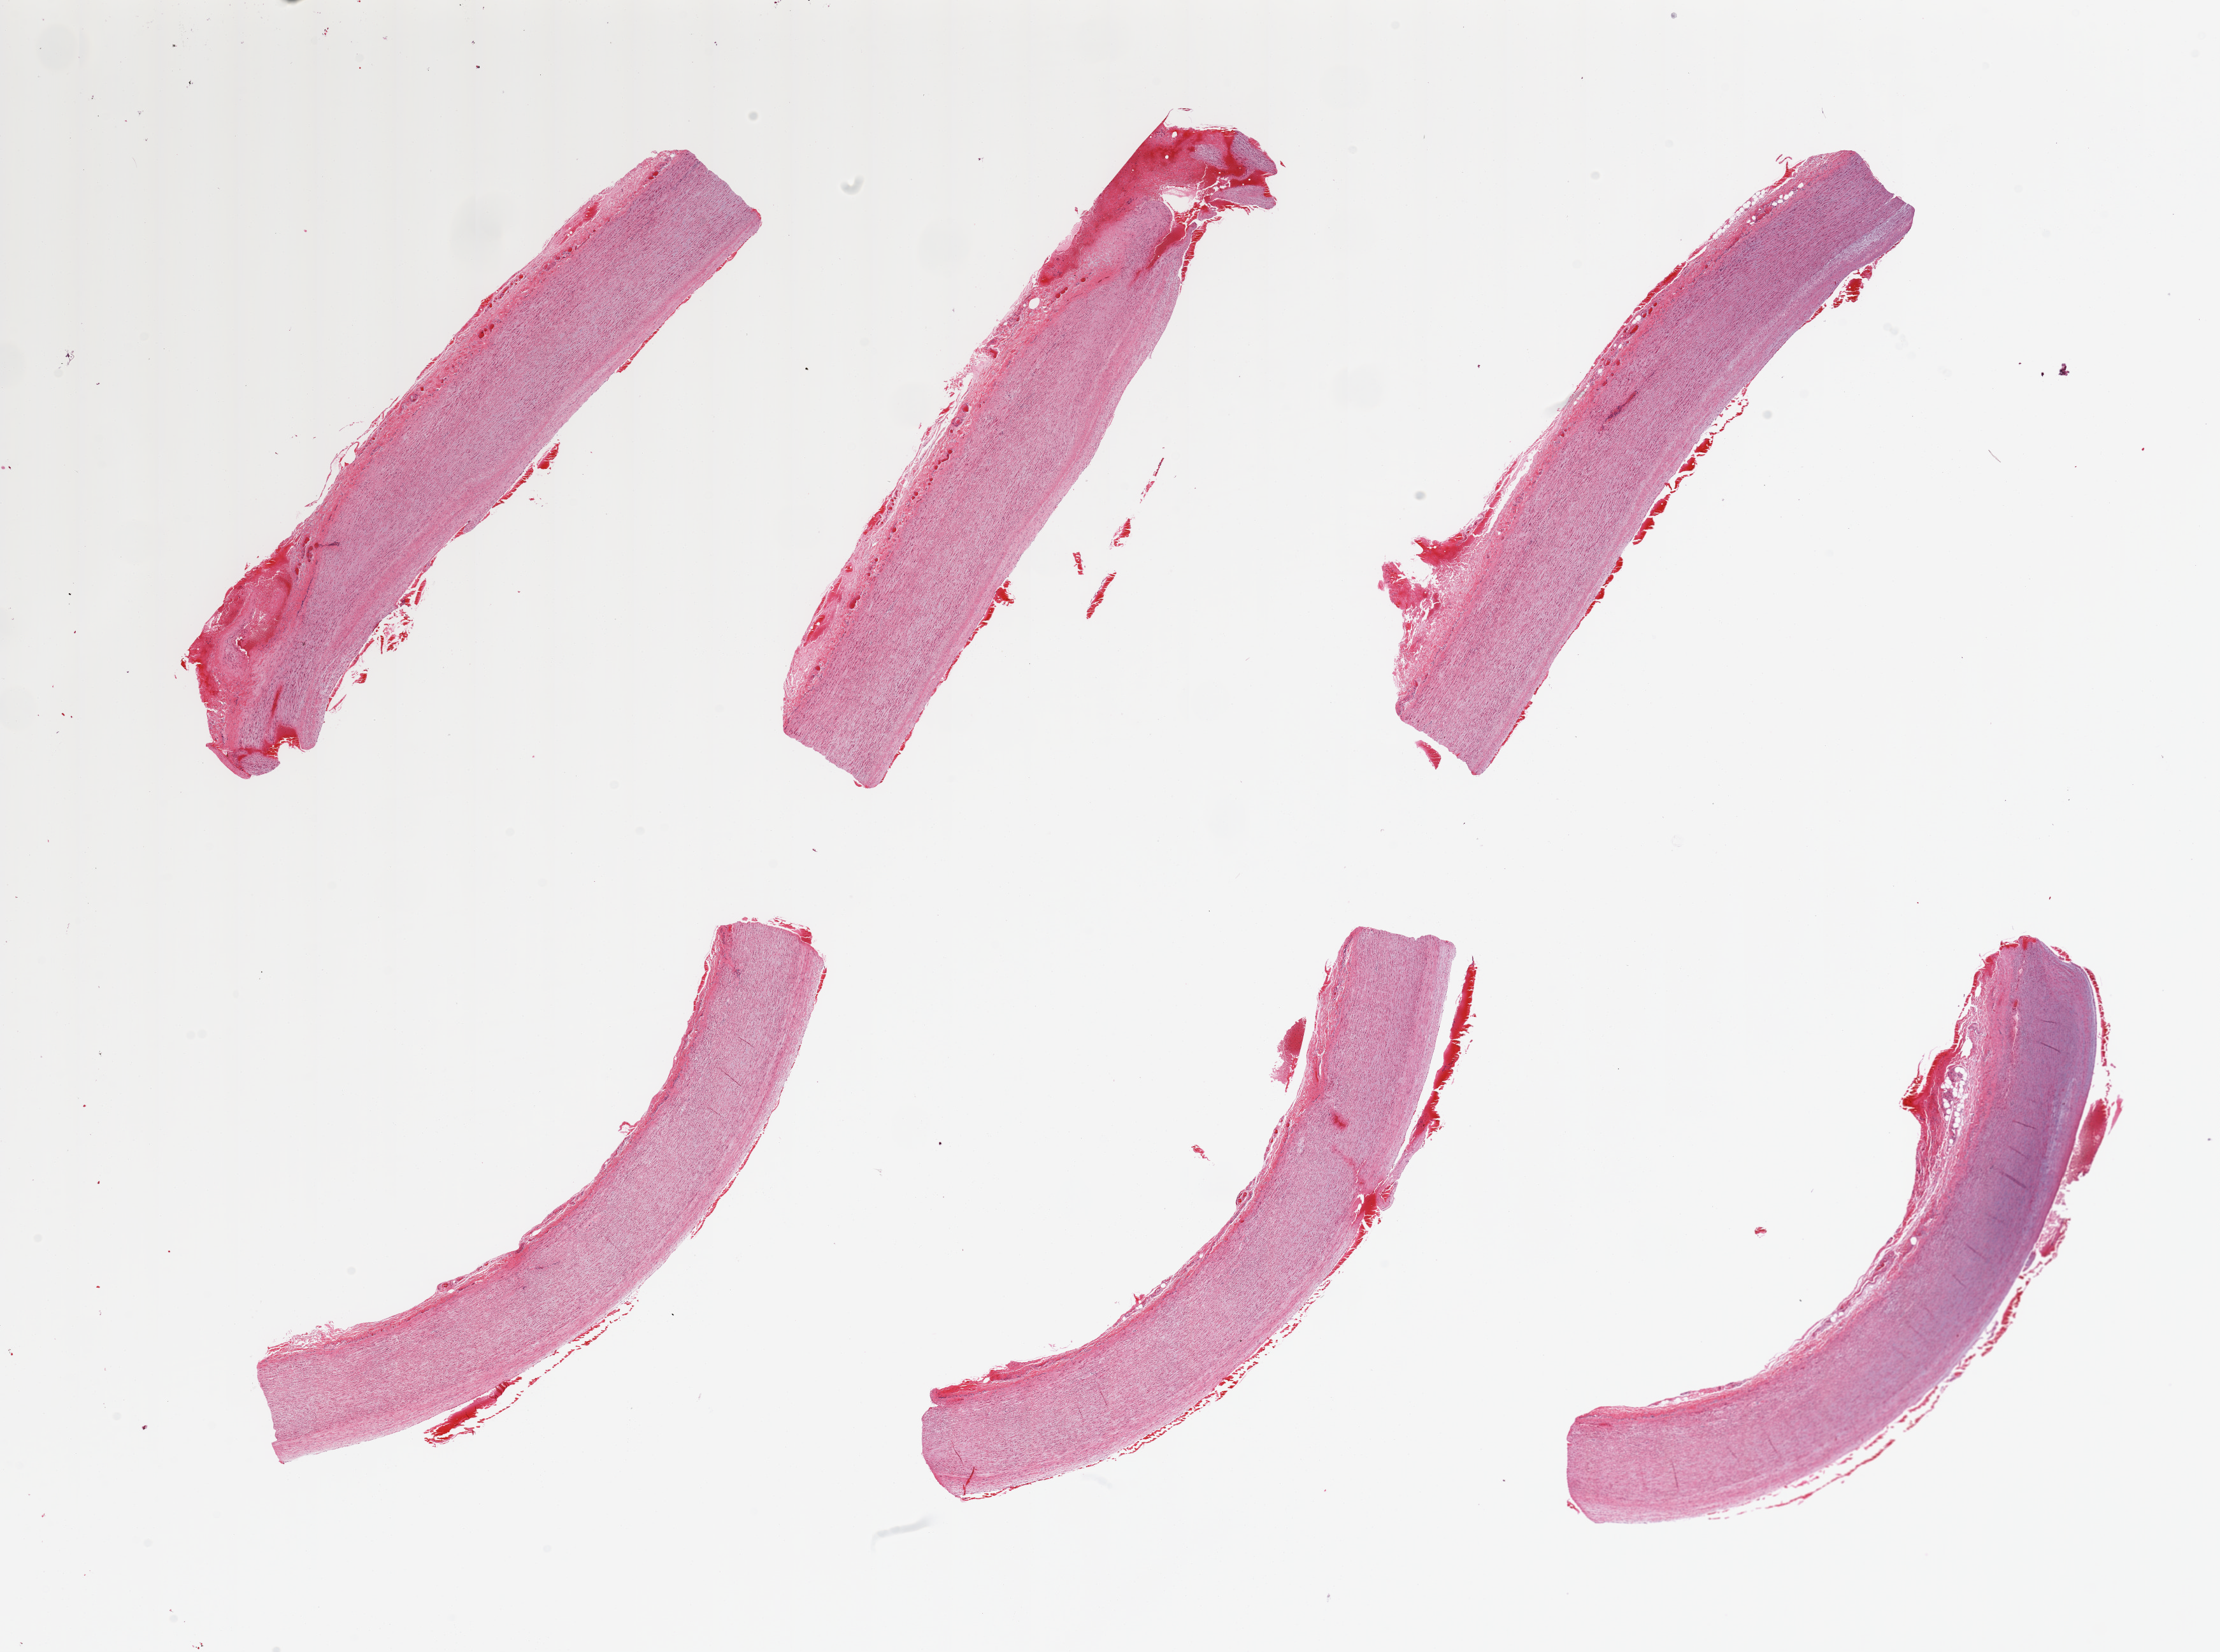
H&E whole-slide image, whole scanned area (about 27.6 x 20.5 mm) shown as a low-resolution overview. PAXgene-fixed paraffin-embedded (PFPE) section. Target tissue: aorta. Tissue donor sample. Female donor.
- review note (as recorded): 6 pieces, adherent congested serosa up to ~1mm